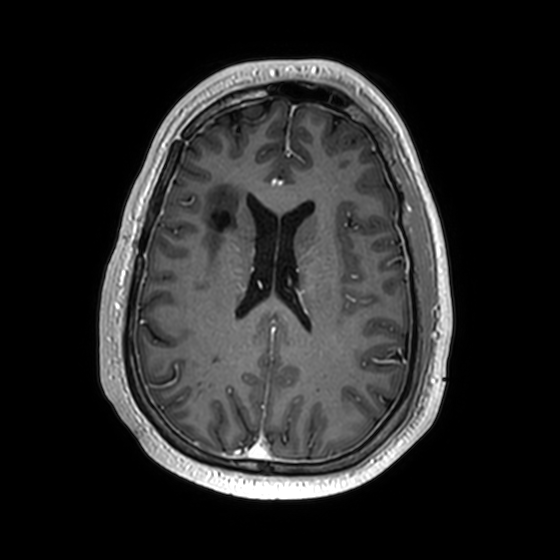
Brain MRI from a brain-tumour surgery series, one axial slice. Position 72 of 174 along the scan axis. T1-weighted post-contrast. 560 × 560 image matrix, field of view 256 × 256 mm. Case-level facts recorded for this patient, not image findings: histopathology: Astrocytoma; WHO grade: 2; IDH mutation: yes; tumour location: Right Insular.
Outlined on this slice (expert manual segmentation):
- previous resection cavity: bounding box <210,210,230,230> (left, top, right, bottom; pixels)